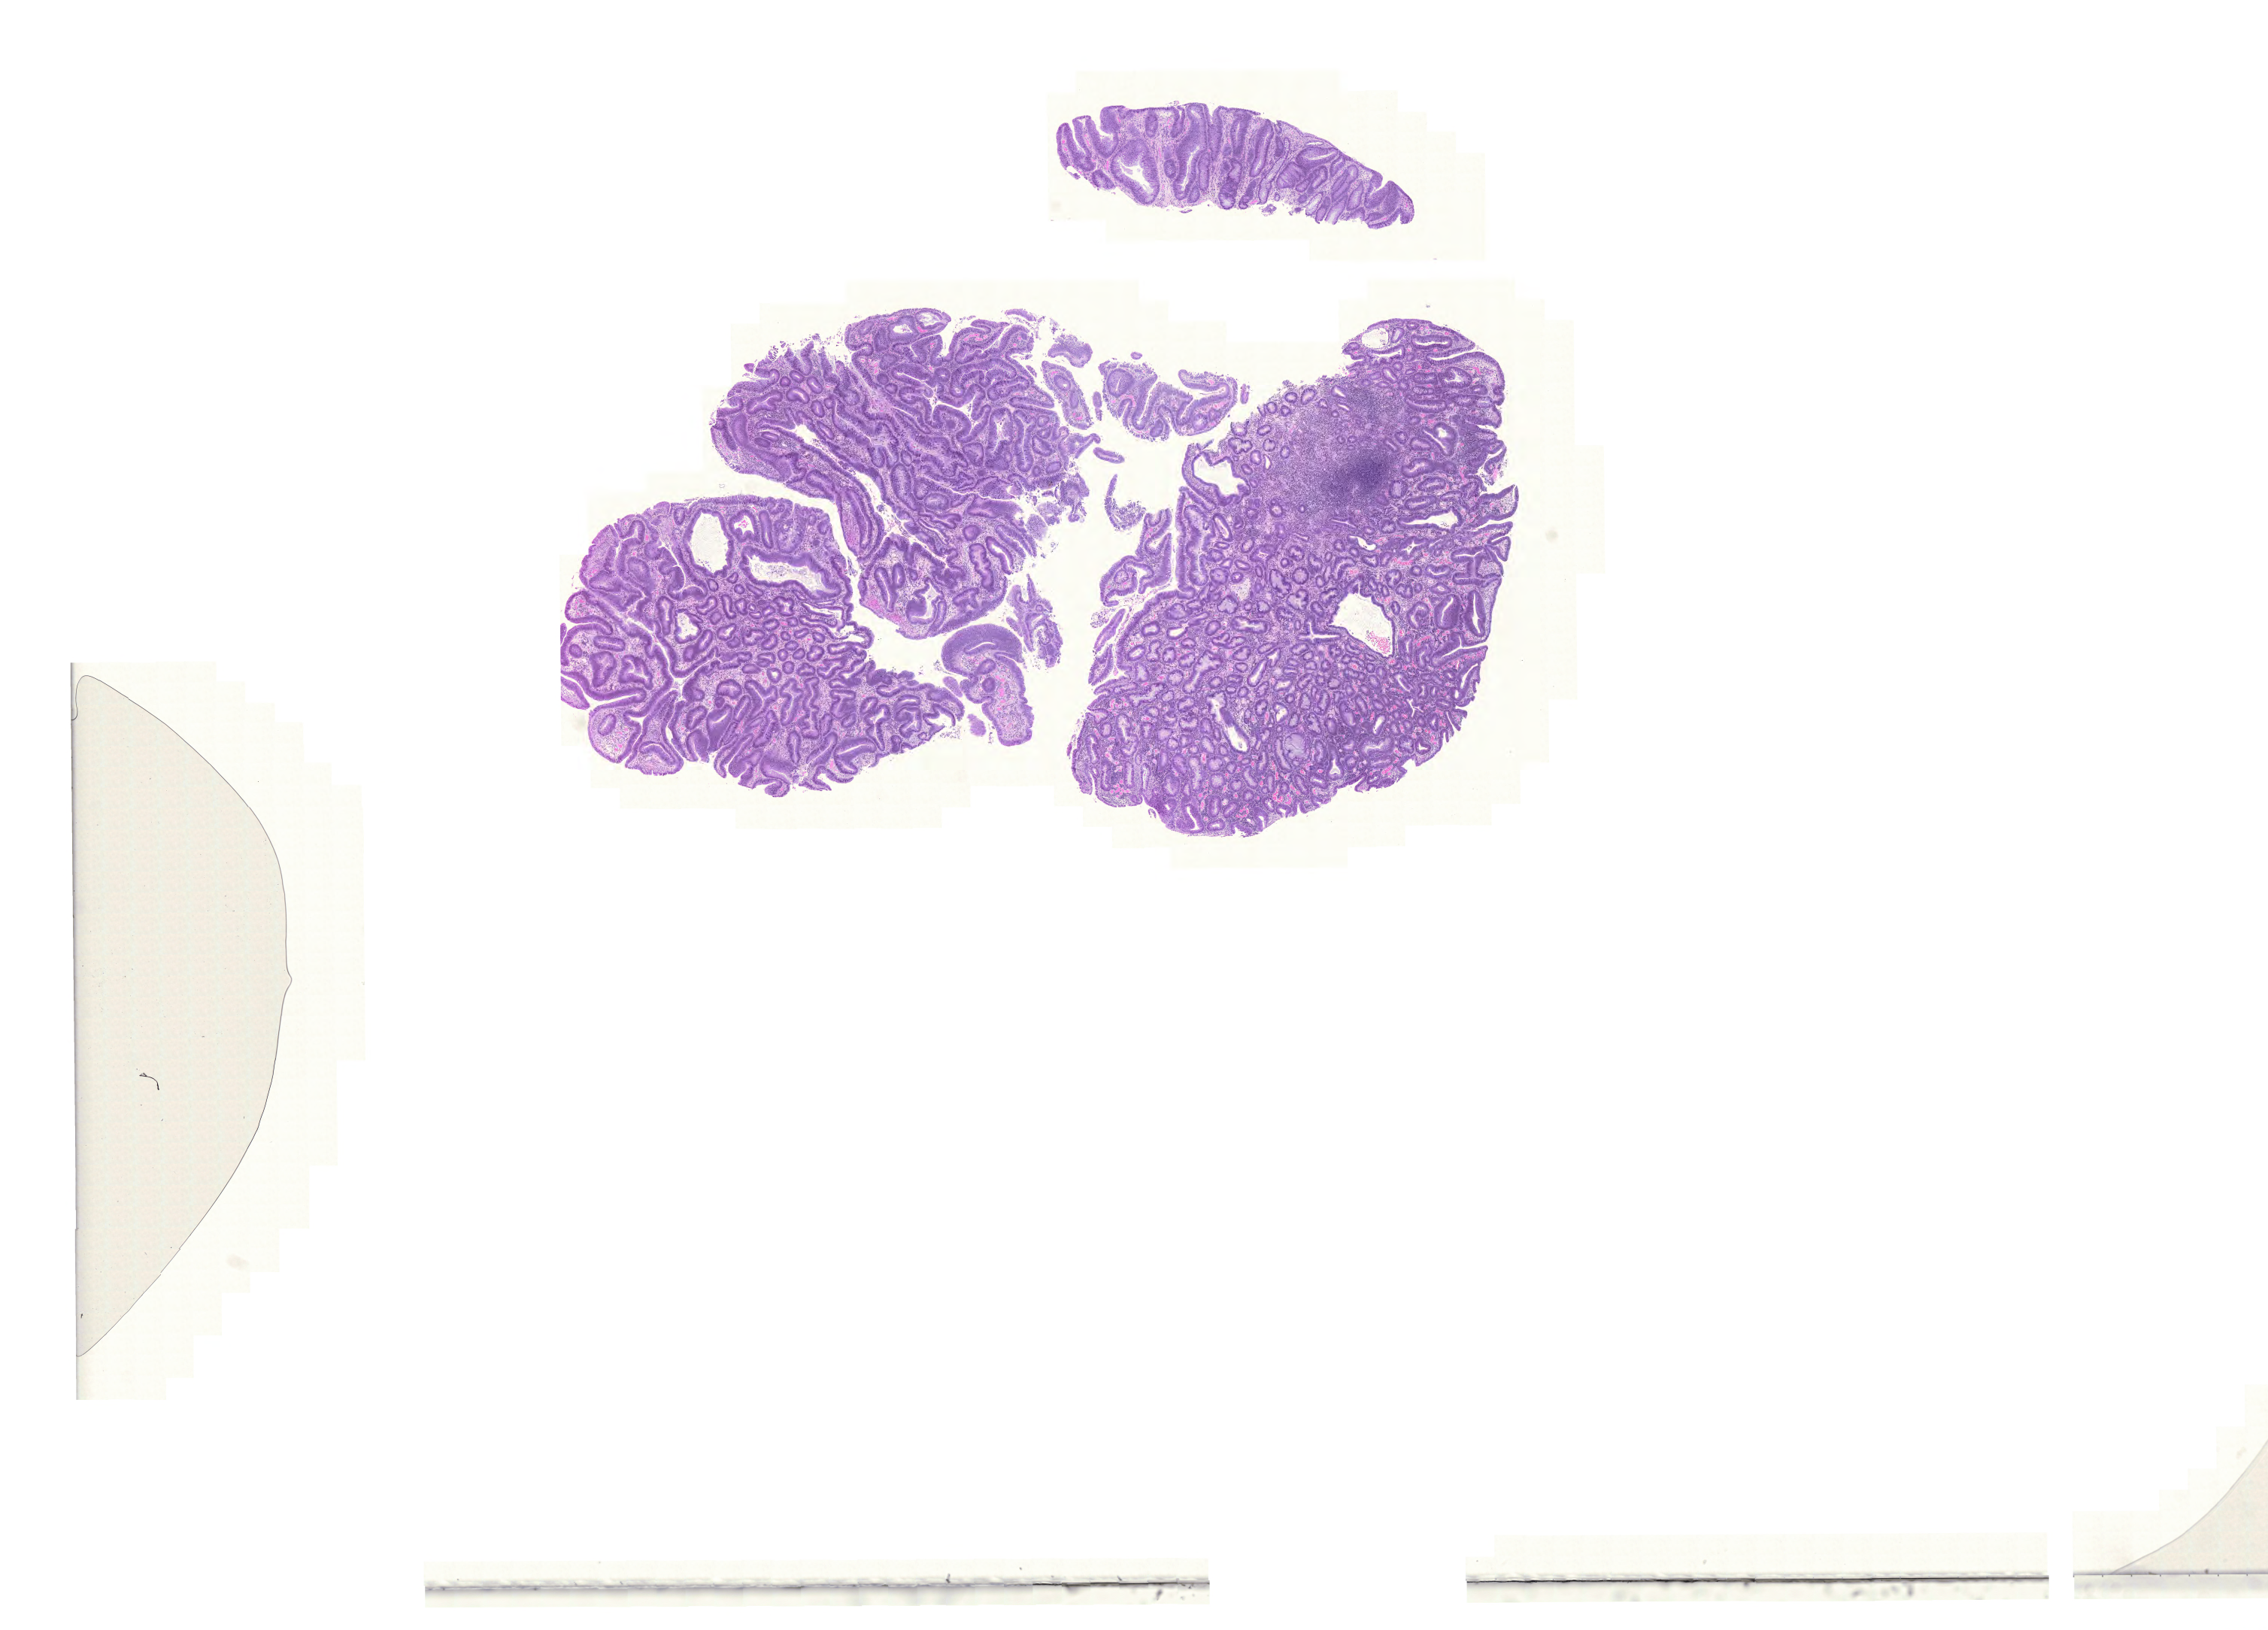
Whole-slide histology image, H&E — whole scanned area (about 22.4 x 16.1 mm, slide scanned at 20x) shown as a low-resolution overview. Formalin-fixed paraffin-embedded (FFPE) diagnostic section. Primary tumour sample from the colon. Male, age 66 years at initial diagnosis.
Histologic diagnosis: Adenocarcinoma, NOS. AJCC pathologic stage: IIA.